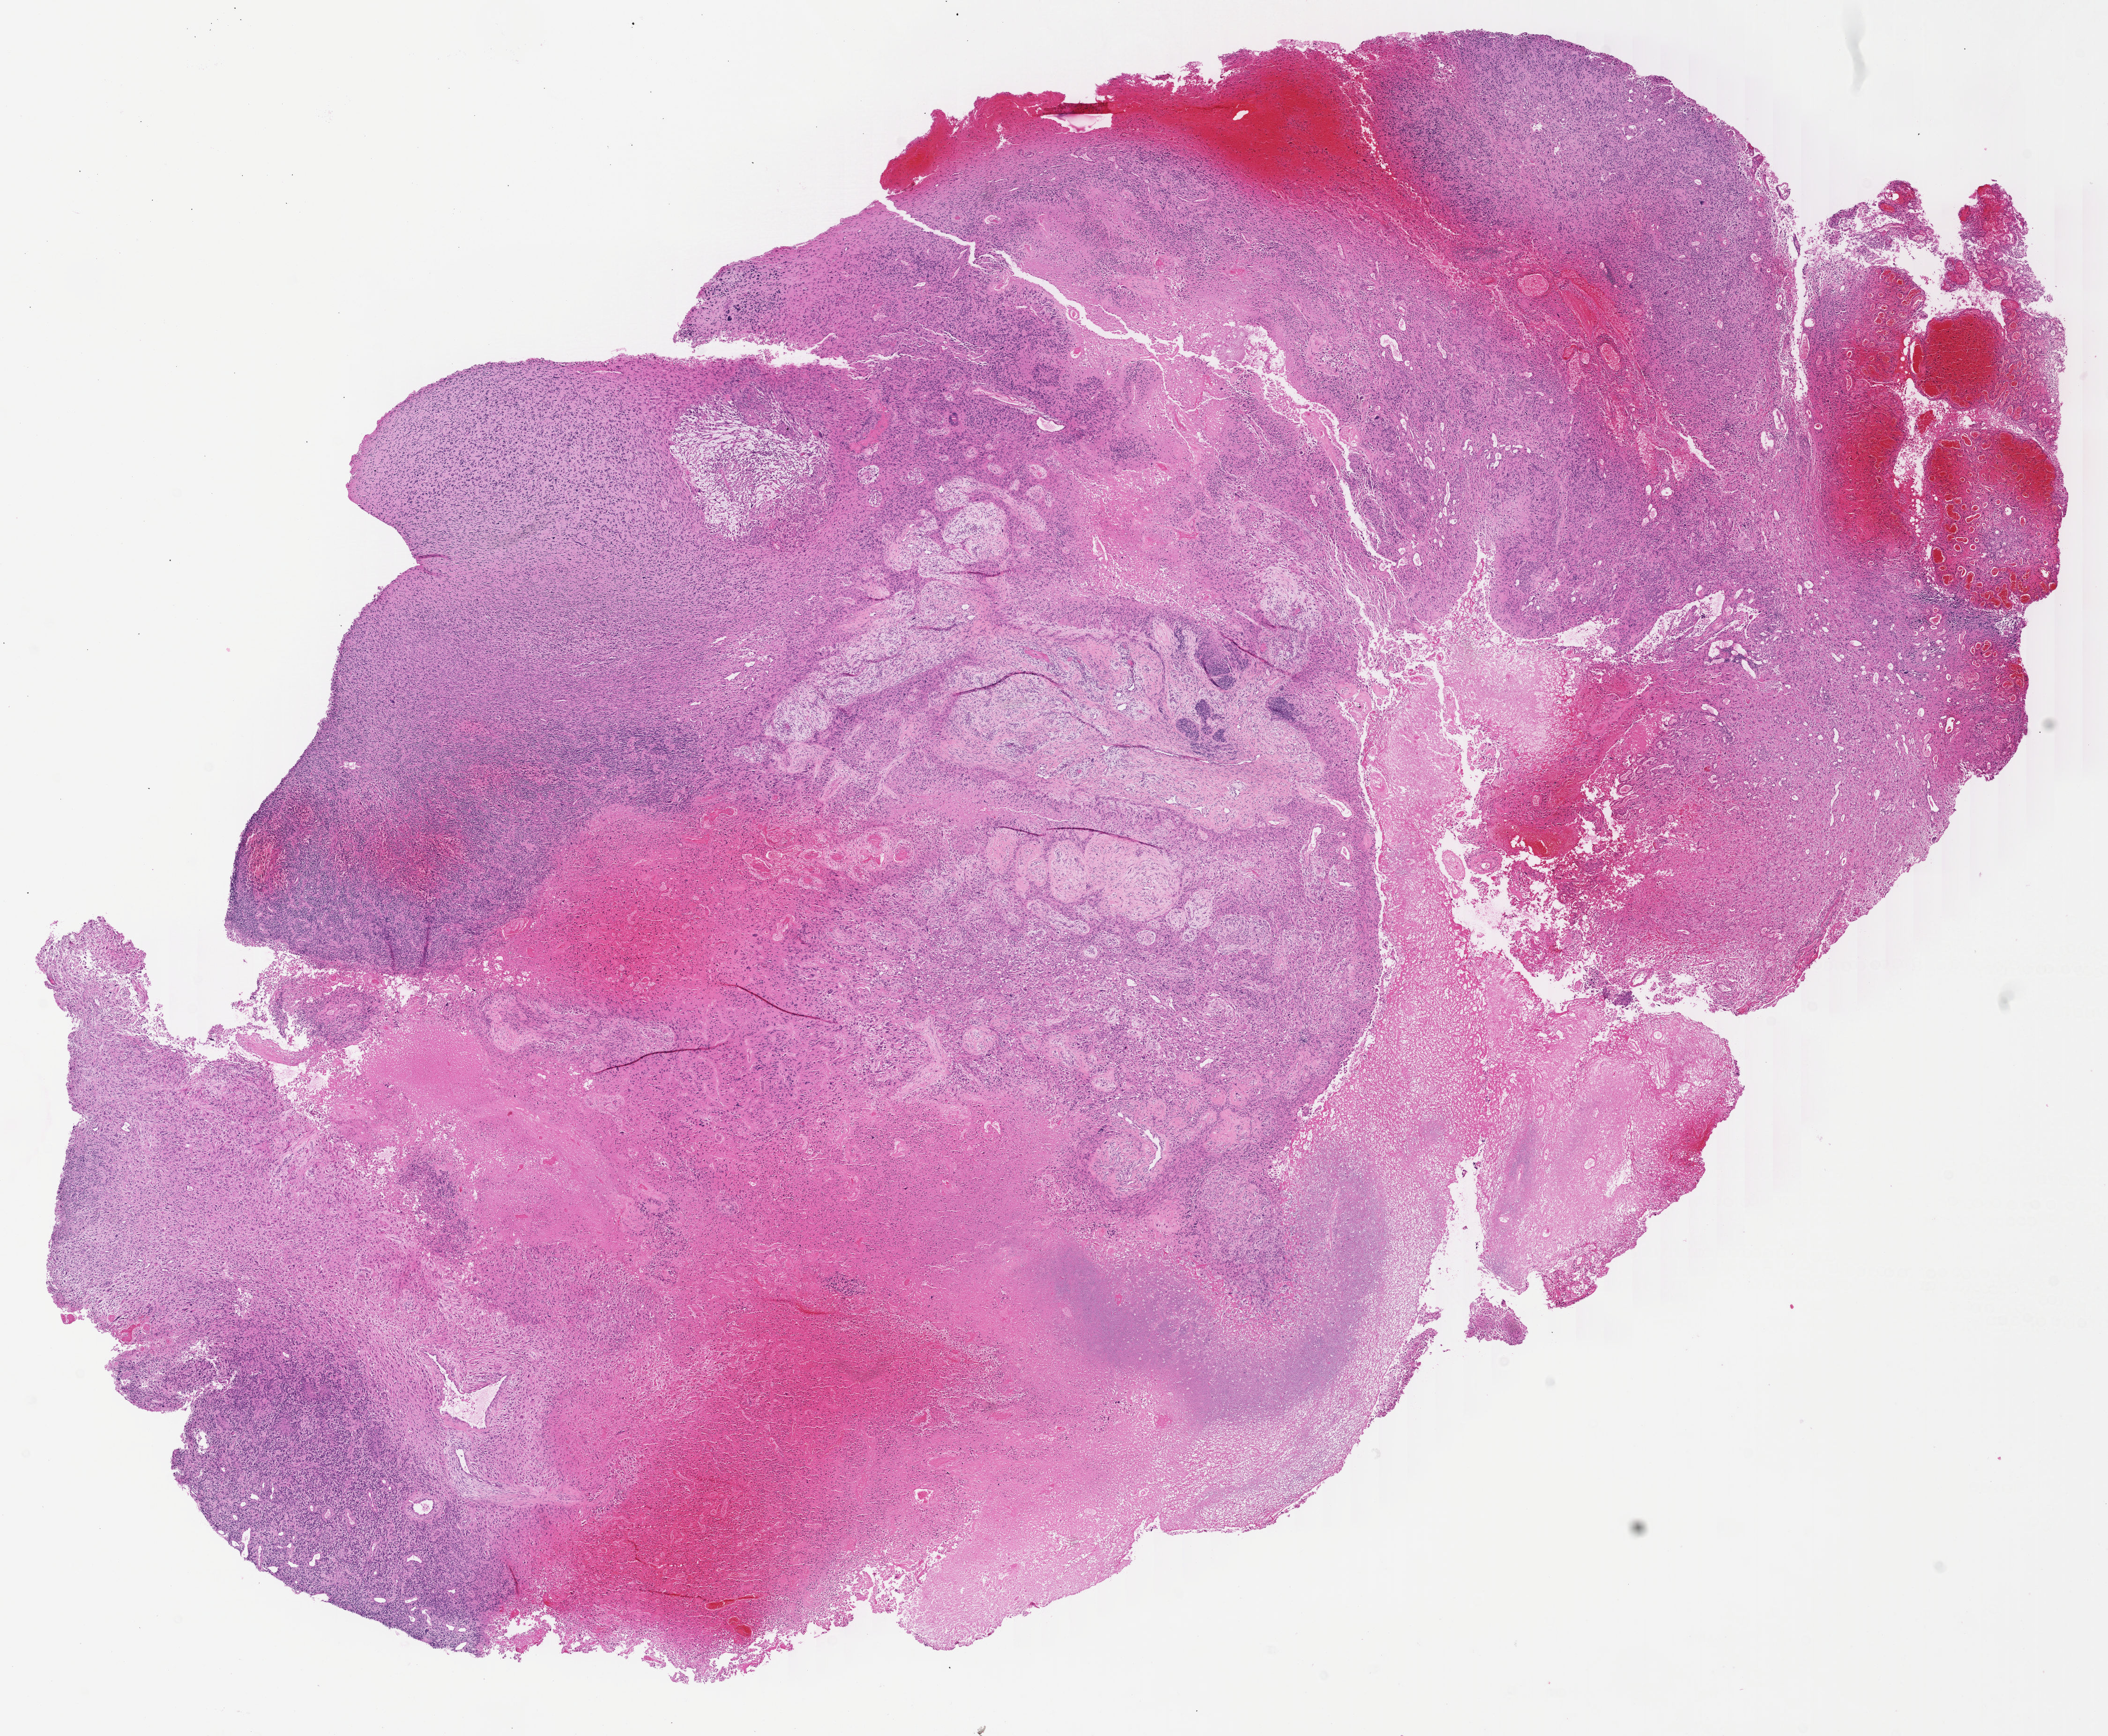
H&E-stained whole-slide image, low-resolution overview of the scanned area, about 18.1 x 14.9 mm, formalin-fixed paraffin-embedded (FFPE) diagnostic section, brain, primary tumour sample. Male patient; age at initial diagnosis 60 years.
Pathologic diagnosis: Glioblastoma.